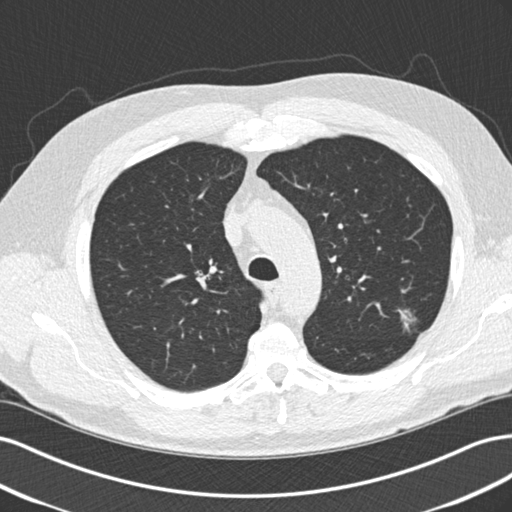
Low-dose screening chest CT, one axial slice. Slice 158 of 209 in the series (ordered by position). Lung window (W 1500 / L -600 HU). 2 mm slice thickness. 512 × 512 image matrix, field of view 360 × 360 mm.
Outlined on this slice (outlined manually by an expert reader):
- lesion 1 (tumor, upper lobe of left lung): box from (x=399, y=310) to (x=414, y=329) px